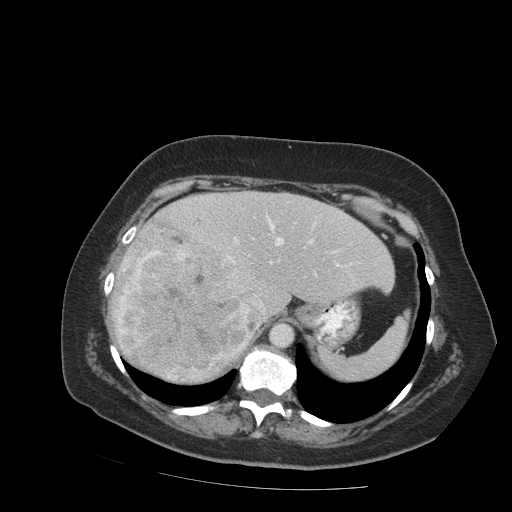
Contrast-enhanced abdominal CT (liver protocol), one axial slice; slice 65 of 99 in the series (ordered by position); reconstruction kernel STANDARD; soft-tissue window (W 400 / L 40 HU); 2.5 mm slice thickness; 512 × 512 image matrix, field of view 400 × 400 mm. Case-level facts recorded for this patient, not image findings: diagnosis: hepatocellular carcinoma (patient treated with transarterial chemoembolisation; whether this scan precedes or follows treatment is not stated here); TNM stage (as recorded): Stage-IVB; Child-Pugh class: A; tumour nodularity: uninodular.
Annotated regions visible in this slice (semi-automatic segmentation, software-assisted and operator-edited):
- abdominal aorta: bounding box (x1, y1, x2, y2) in pixels: (269, 323, 293, 348)
- liver parenchyma outside the tumour (the mass and vessels are separate outlines, so this box may not span the whole liver): (112, 190, 394, 382)
- mass: (112, 224, 260, 383)
- liver vessels: (227, 214, 352, 313)